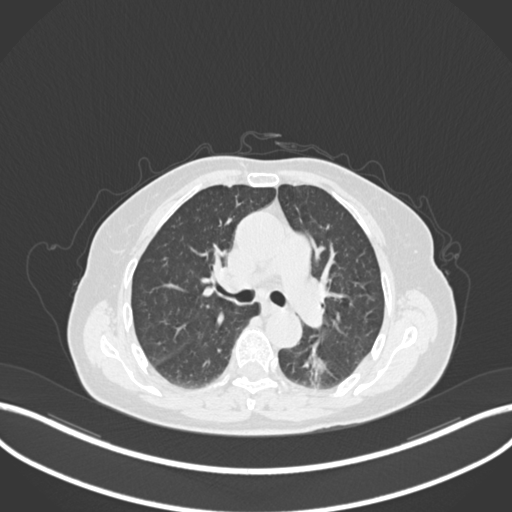
Chest CT, one axial slice; position 530 of 727 along the scan axis; reconstruction kernel B30f; 120 kVp; lung window (W 1500 / L -600 HU); 512 × 512 image matrix, field of view 400 × 400 mm. Female patient, age 70 years. From the clinical record (not read from this slice): clinical TNM (as recorded): T1c N0 M0.
Outlined on this slice (bounding box drawn by a radiologist):
- lung tumour (recorded histology: adenocarcinoma): bounding box <303,341,326,386> (left, top, right, bottom; pixels)